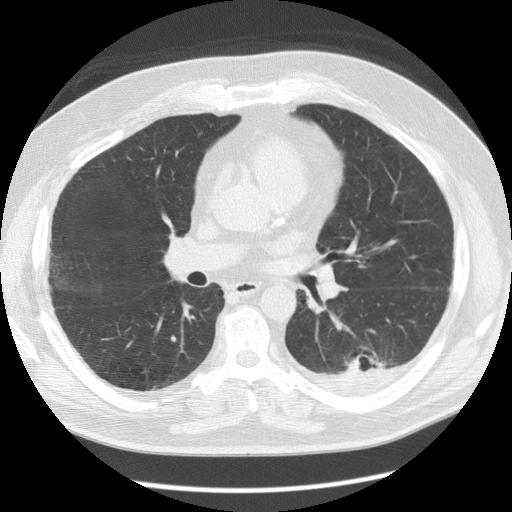
Low-dose screening chest CT, one axial slice. Reconstruction kernel STANDARD. Lung window (W 1500 / L -600 HU). 2.5 mm slice thickness. 512 × 512 image matrix.
Structures marked on this image (expert manual segmentation):
- lesion 1 (tumor, lower lobe of left lung): bounding box (x1, y1, x2, y2) in pixels: (347, 355, 381, 373)